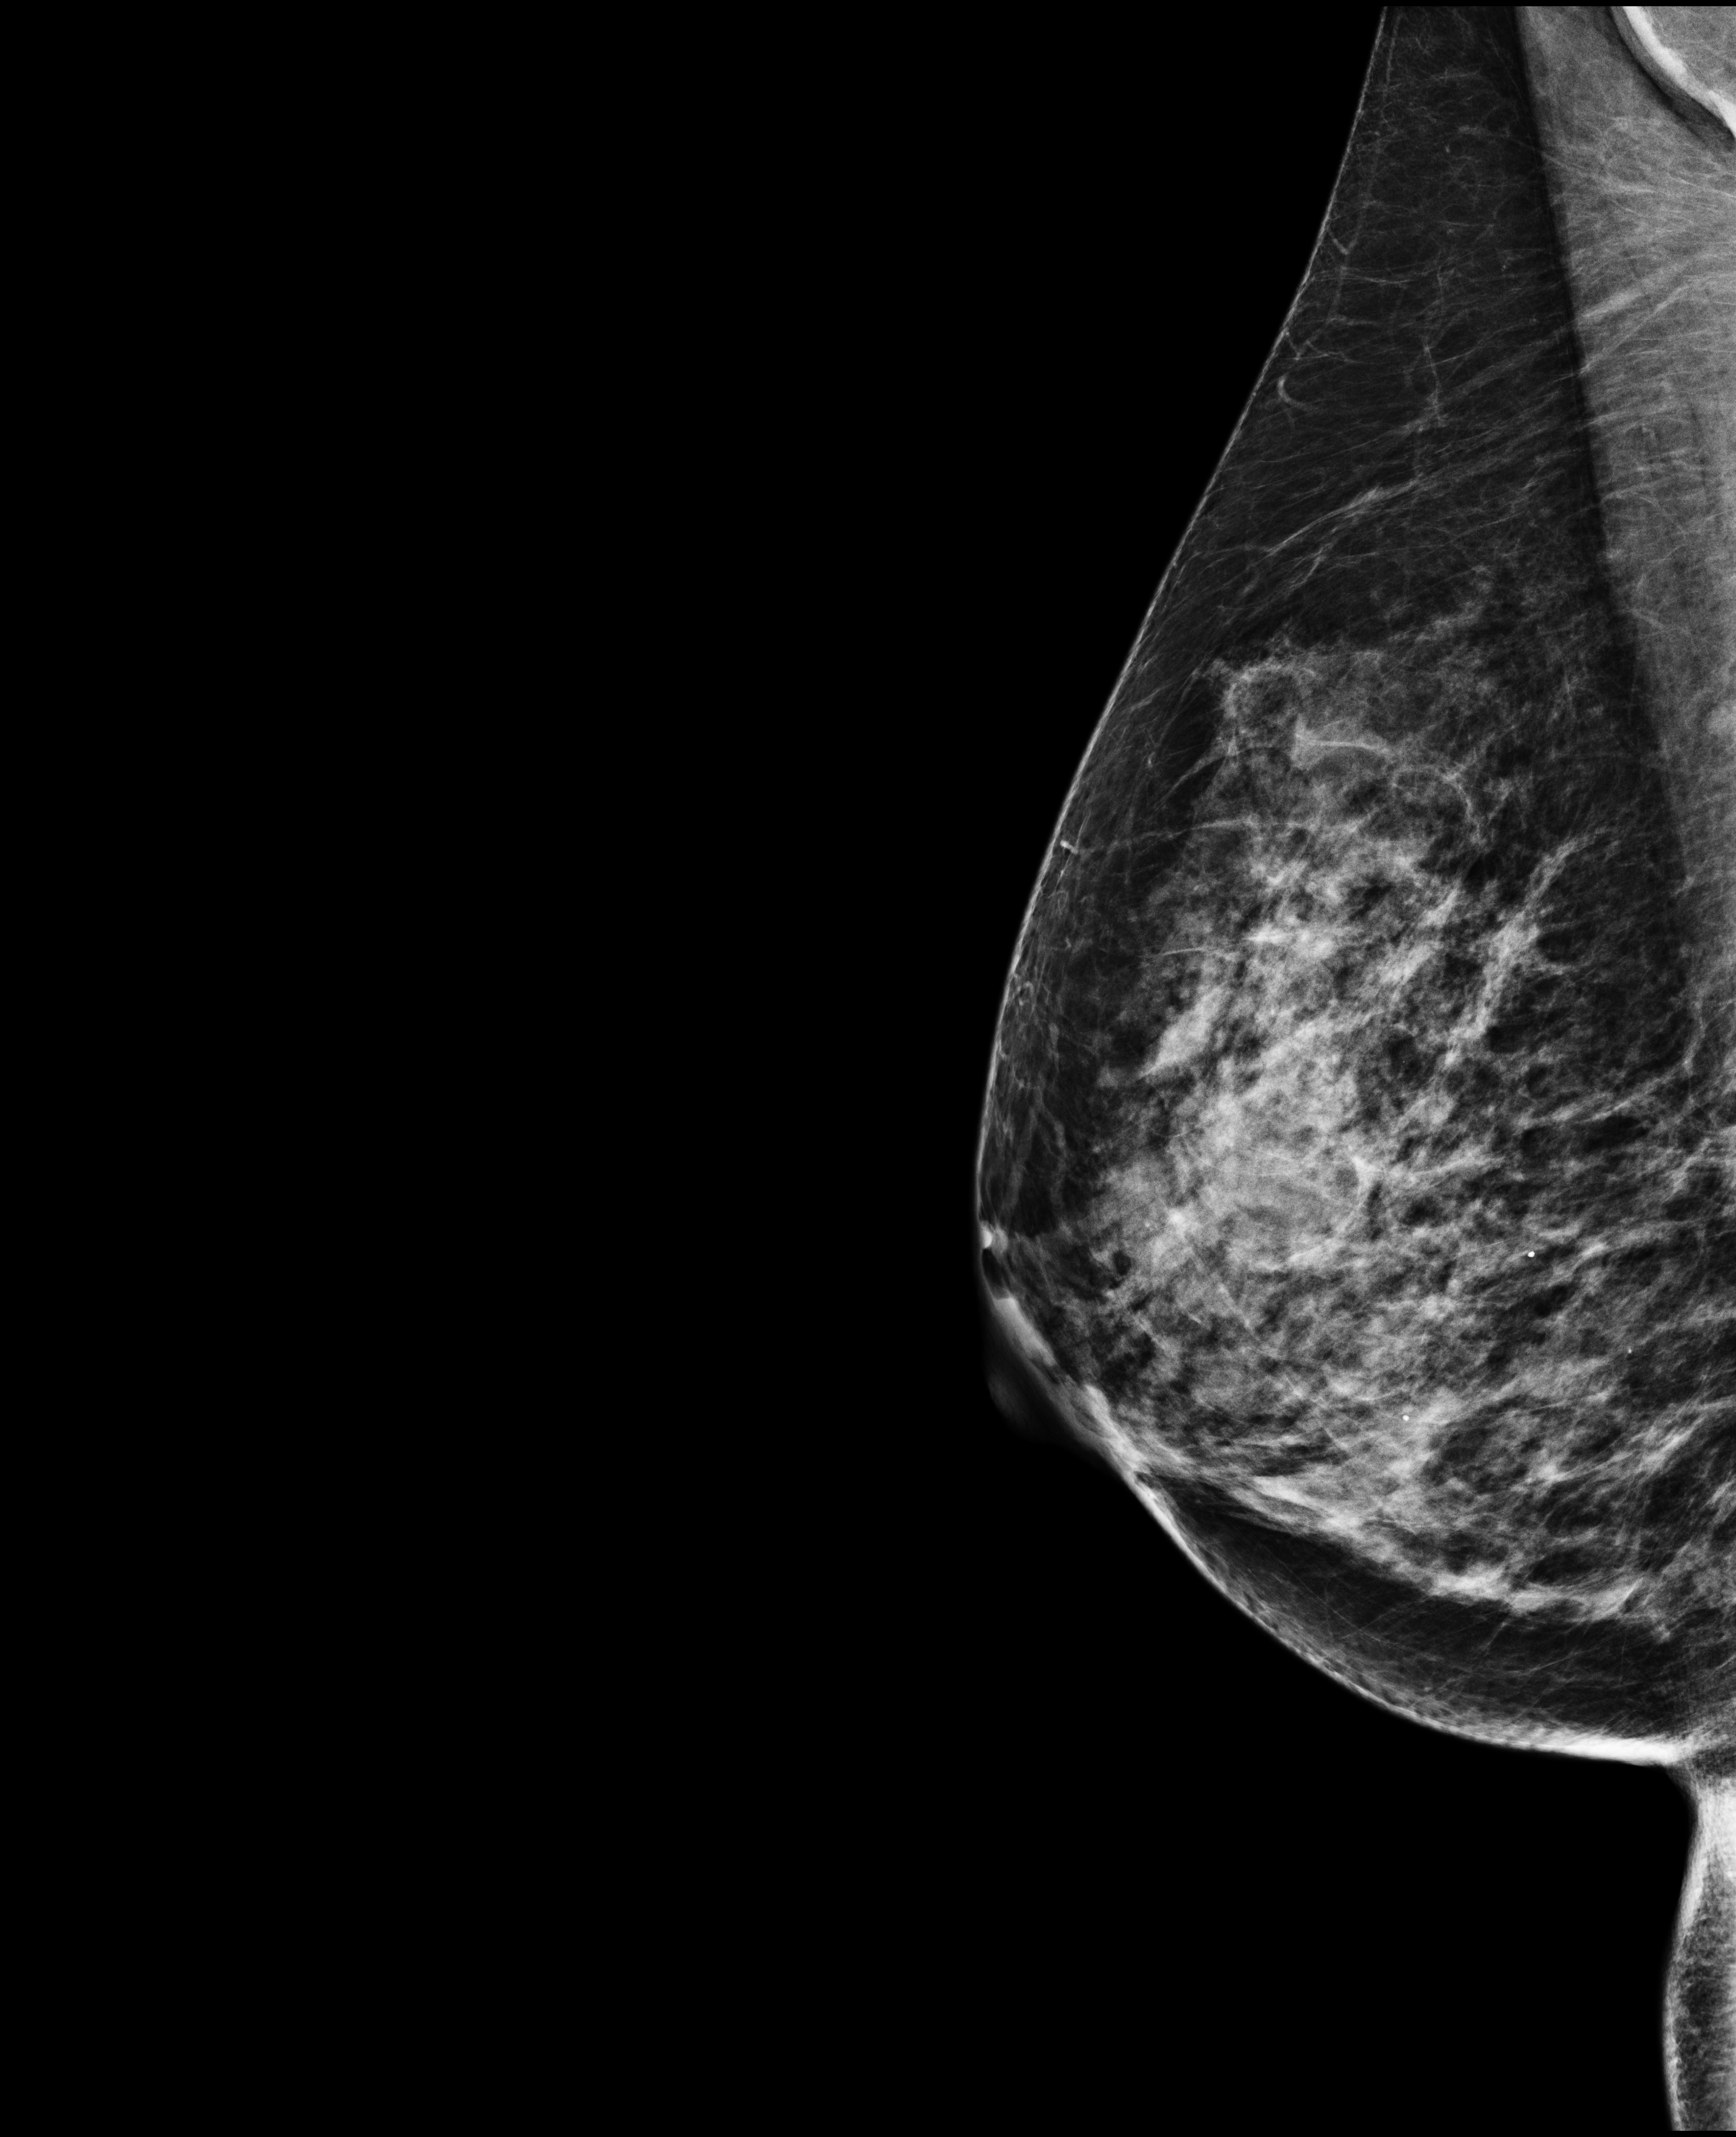
Screening examination, system: Selenia Dimensions. Patient aged 47 years (female).
Image type: full-field digital mammogram. Breast: right. Projection: medio-lateral oblique projection.